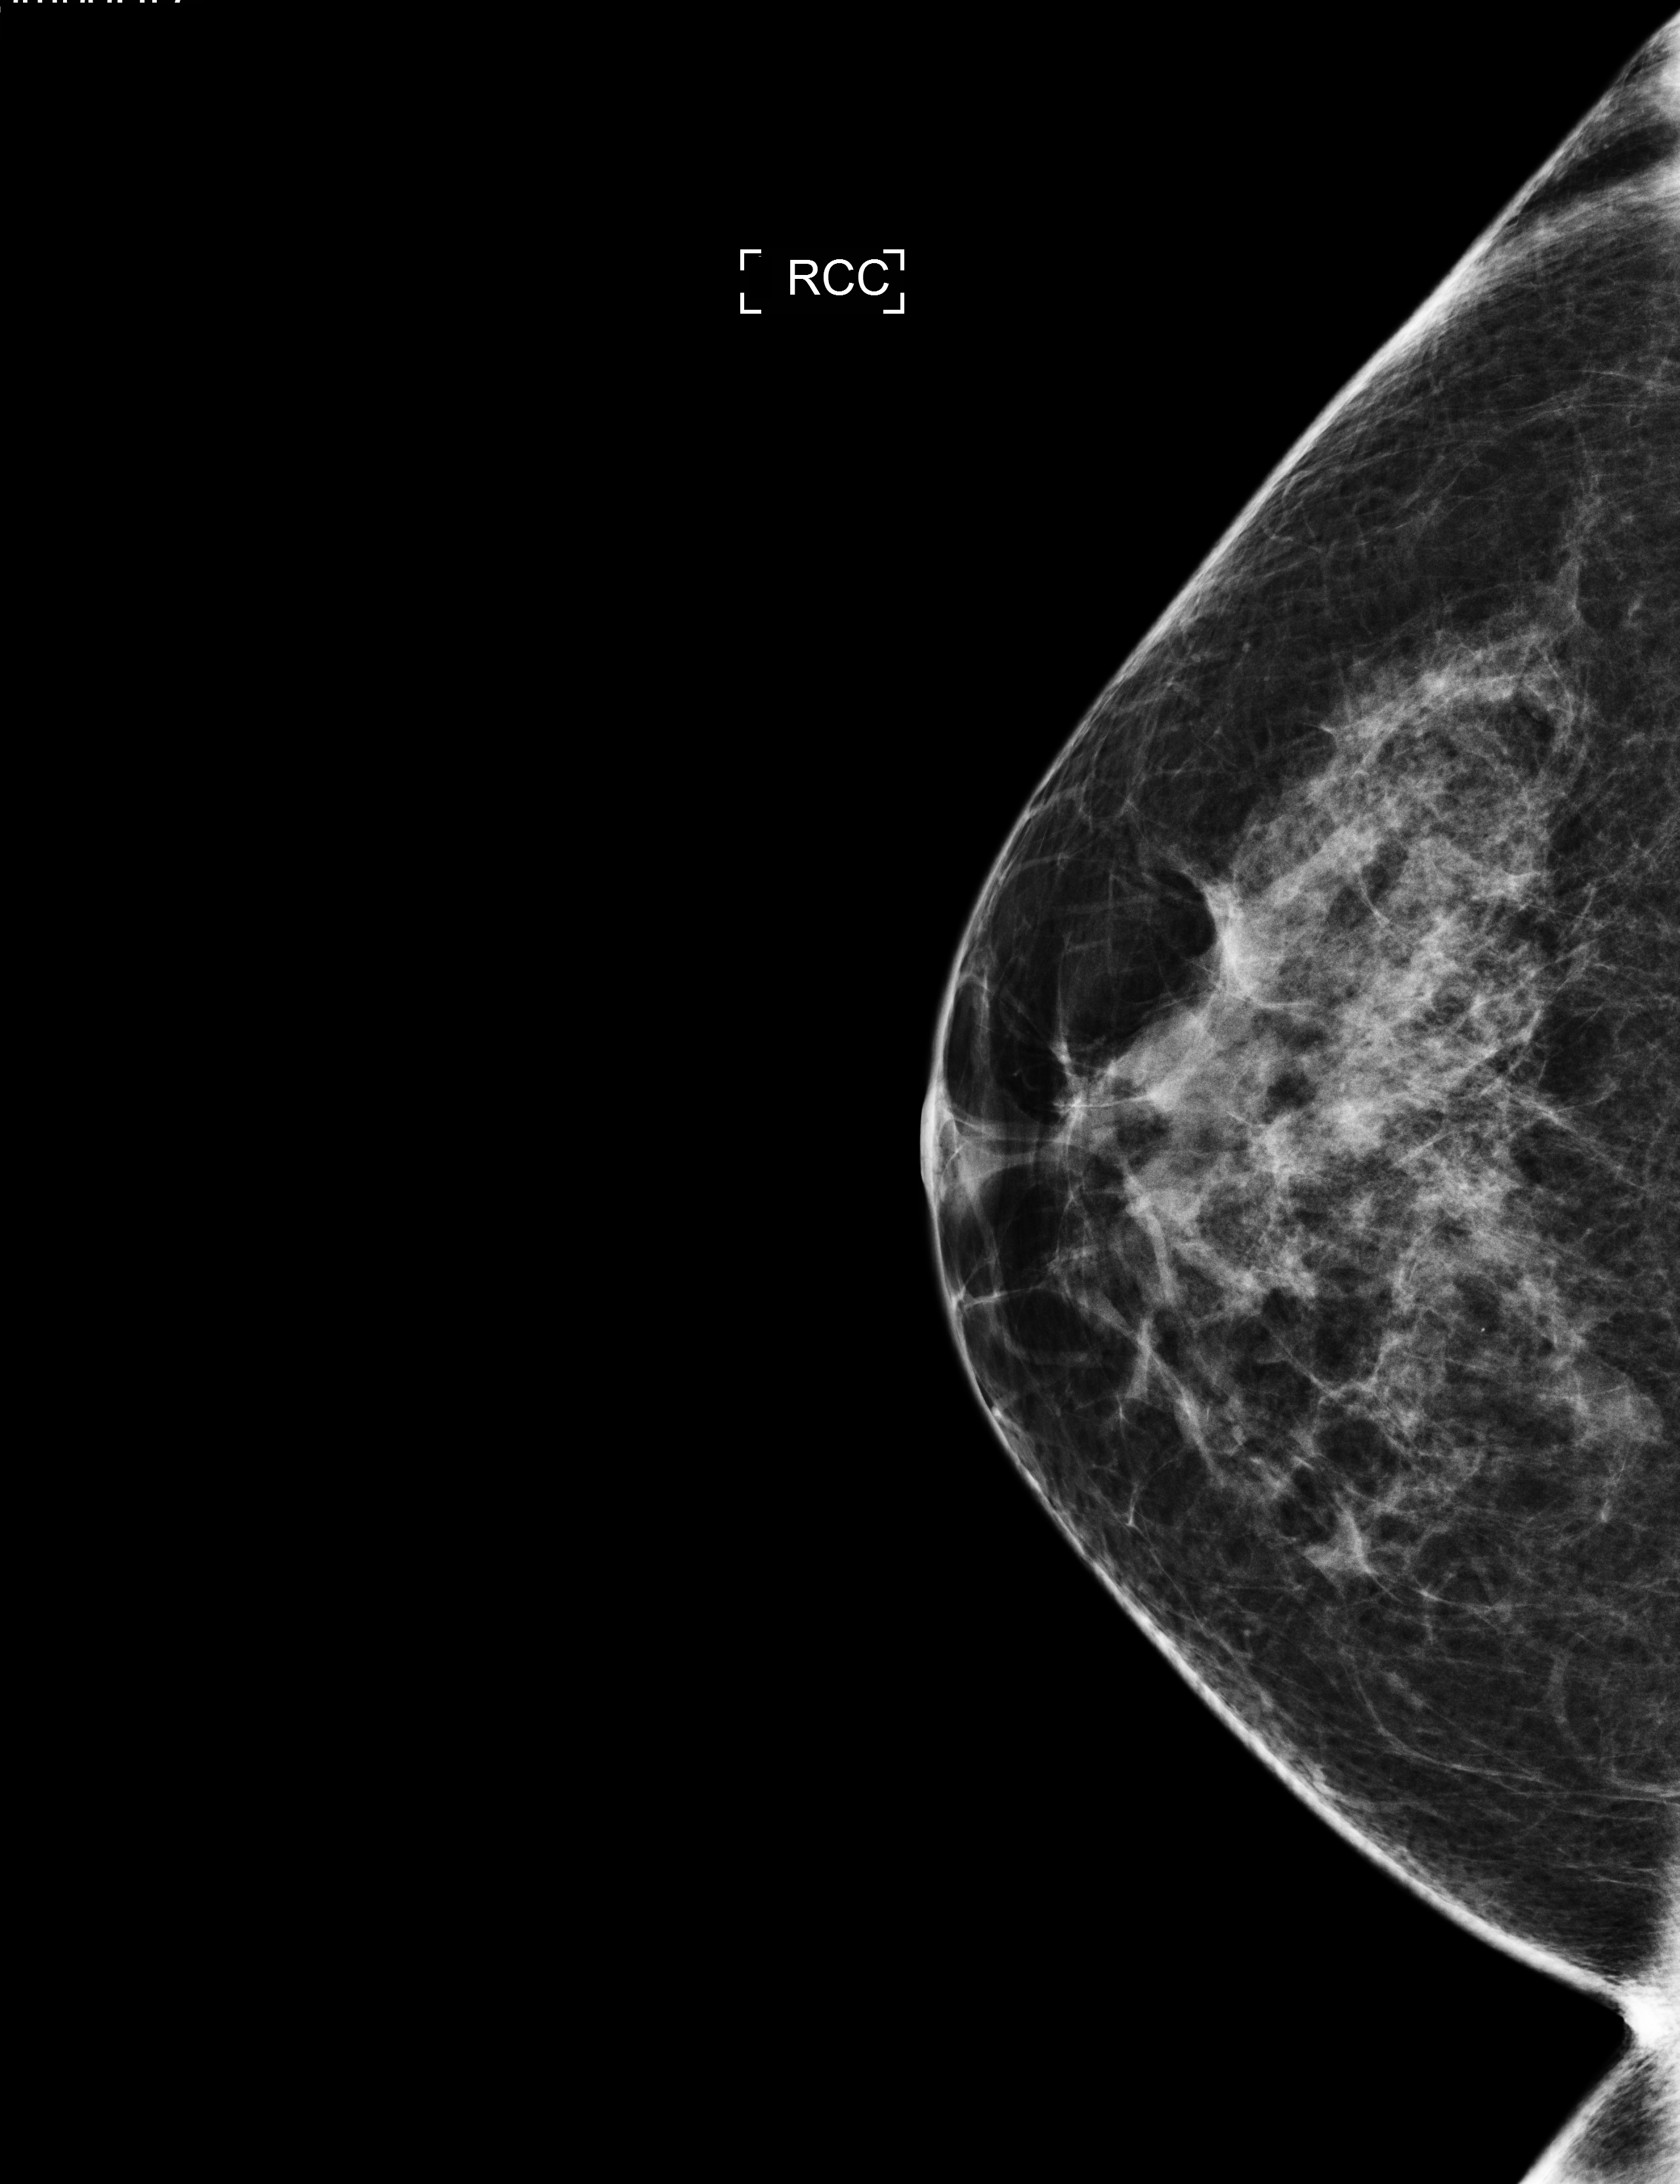
Full-field digital mammogram (FFDM); right breast; cranio-caudal projection; annual screening mammography examination; system: Selenia Dimensions. Female patient, age 44 years.
Breast density at the screening exam (both breasts): heterogeneously dense (BI-RADS density category c). Final BI-RADS category for the screening round (tomosynthesis exam, both breasts): category 1. Recall: no recall after this screen.